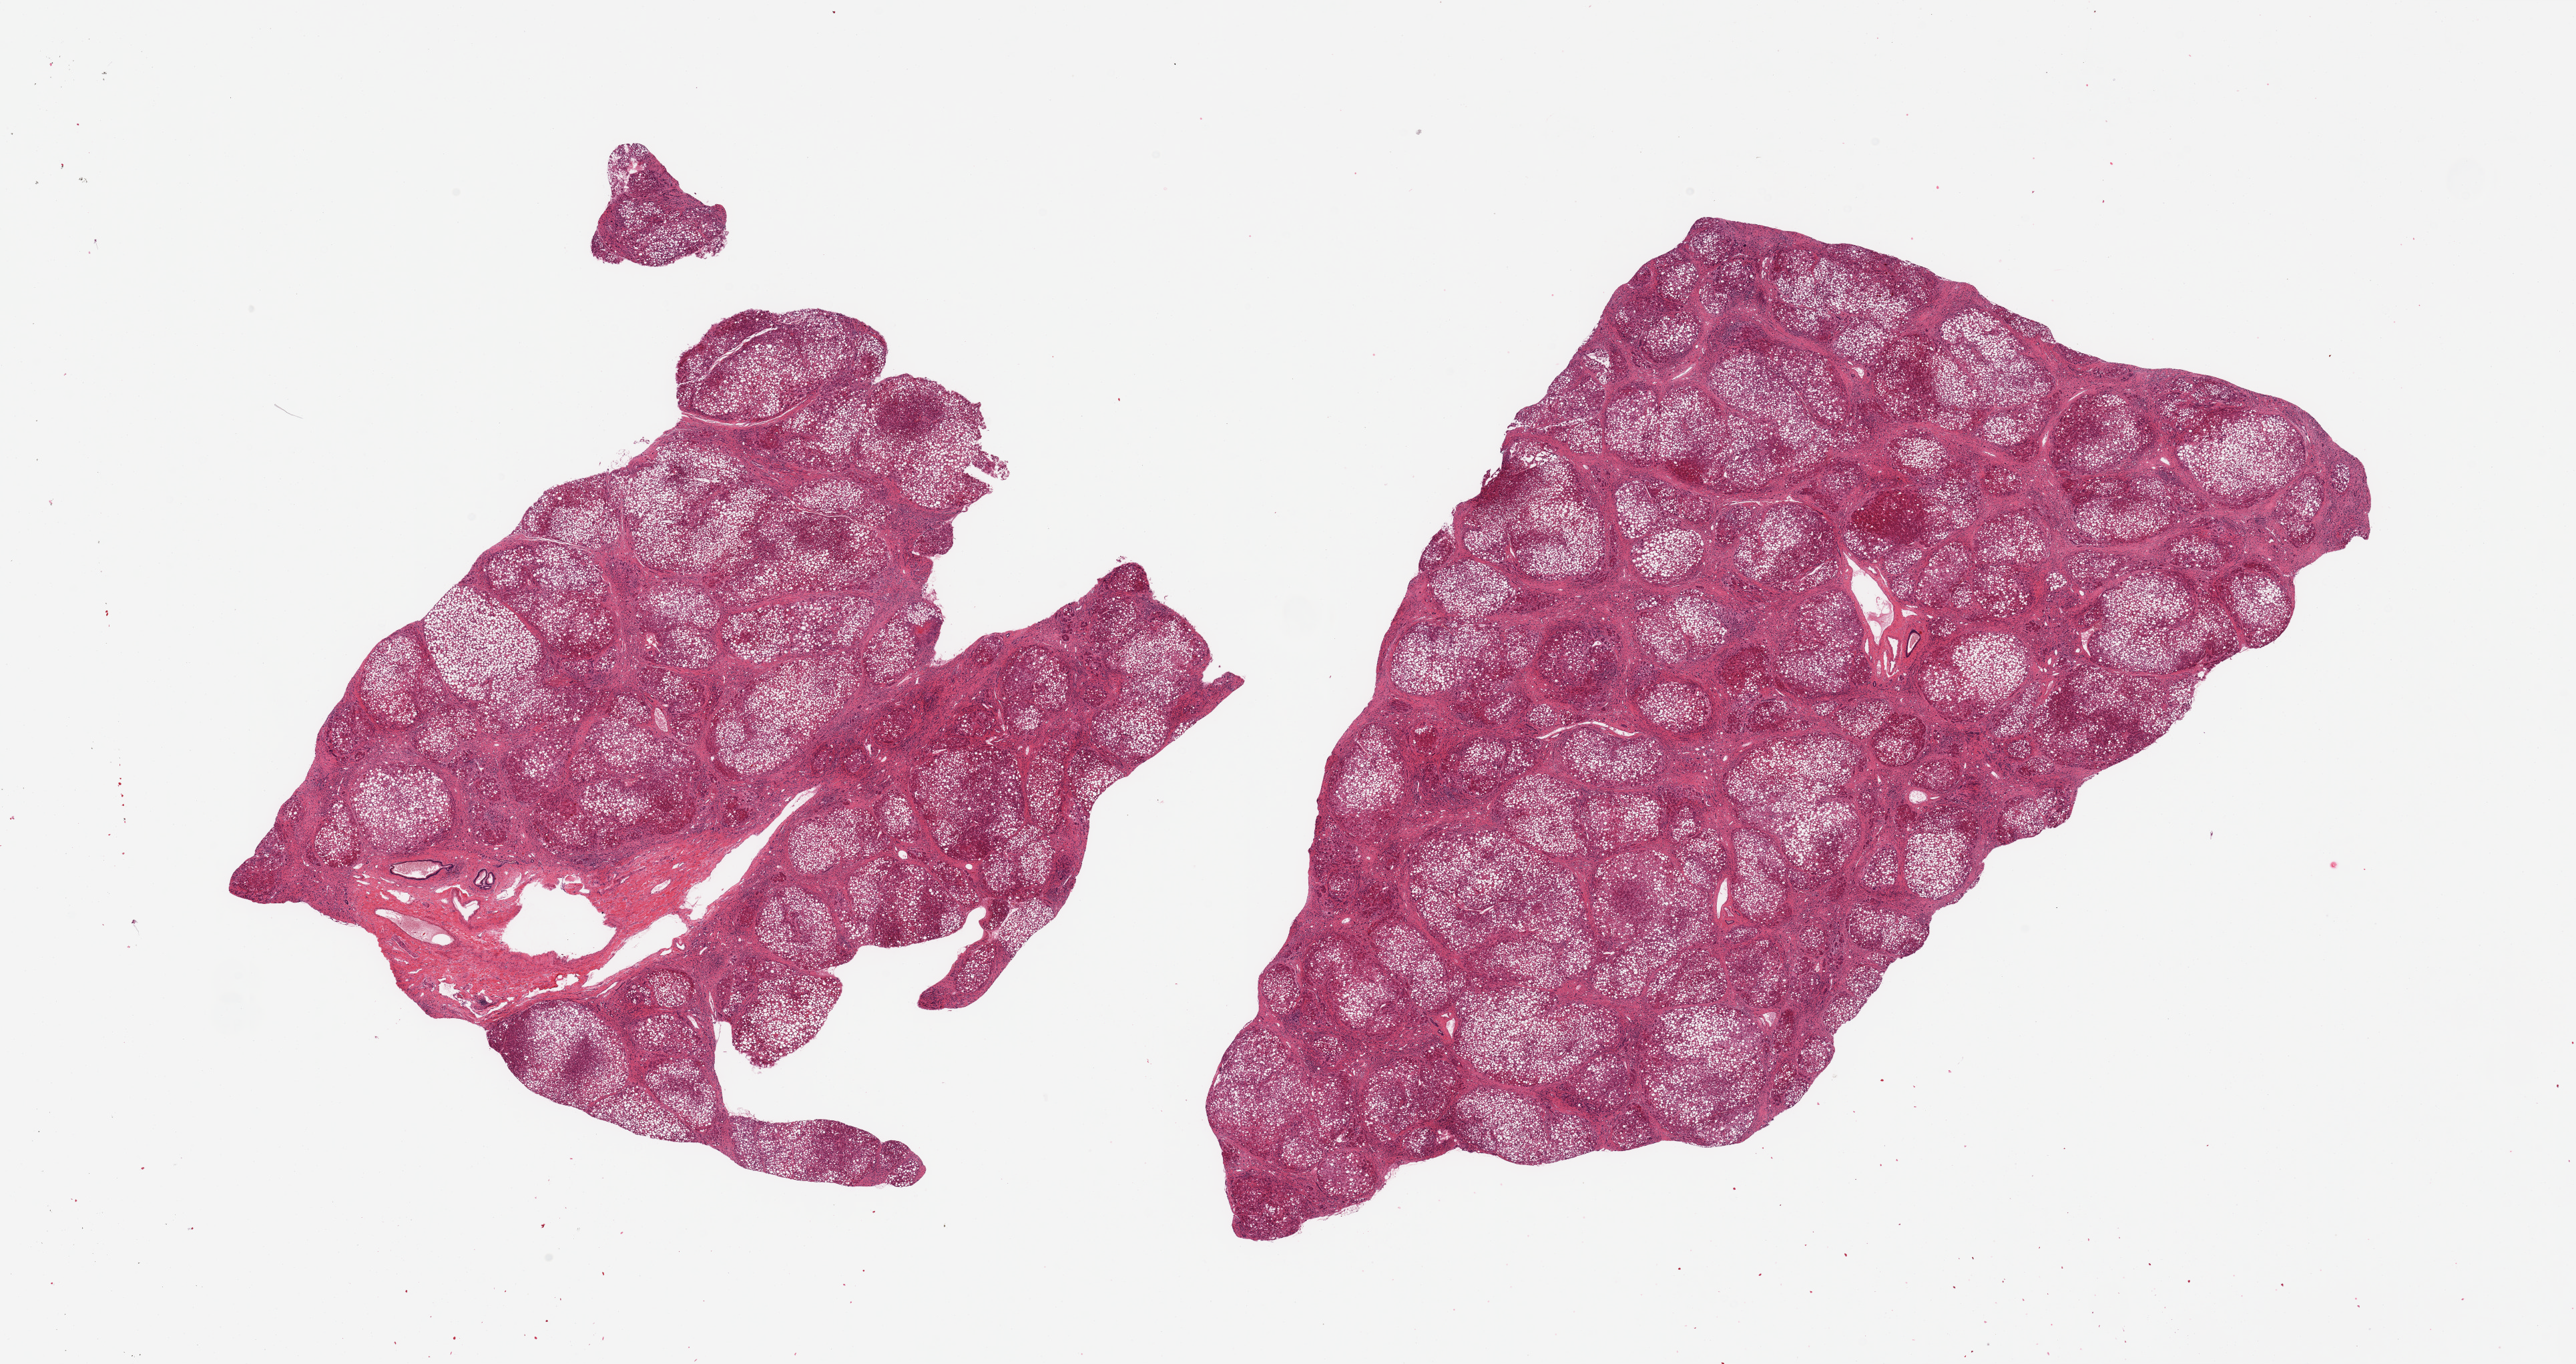
Hematoxylin and eosin (H&E) whole-slide image, whole scanned area (about 30.5 x 16.2 mm) shown as a low-resolution overview; PAXgene-fixed, paraffin-embedded tissue; section of liver (target tissue); donor tissue sample. Donor: female.
Reviewer comment on this tissue sample: 2 pieces established cirrhosis with diffuse marked macrovesicular steatosis.